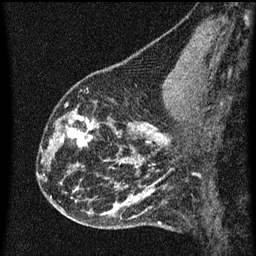
Breast MRI (dynamic contrast-enhanced), one sagittal slice. Slice 22 of 60 in the series (ordered by position). Dynamic contrast-enhanced series, image 2 of 3 at this slice position (ordered by acquisition). 1.5 T. TE 4.2 ms, TR 8 ms. 256 × 256 image matrix. Female patient, age 43 years.
Structures marked on this image (semi-automatic segmentation, software-assisted and operator-edited):
- analysis volume of interest (the breast-tissue region the enhancement analysis was run in; not a lesion): box from (x=55, y=104) to (x=104, y=153) px
- tumour enhancement mask (voxels above the 70 % enhancement threshold inside the analysis volume of interest): (x=60, y=114)–(x=98, y=147)